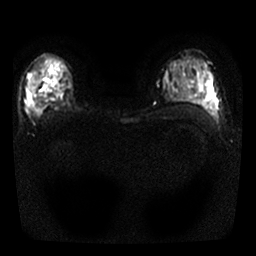
Breast MRI, one axial slice; slice 16 of 25 in the series (ordered by position); diffusion-weighted series; image 2 of 4 stored at this slice position (different b-values; order by instance number); 1.5 T; 256 × 256 image matrix, field of view 300 × 300 mm. Female patient.
Annotated regions visible in this slice (expert manual segmentation):
- tumour on diffusion-weighted imaging: bounding box (x1, y1, x2, y2) in pixels: (26, 93, 39, 112)